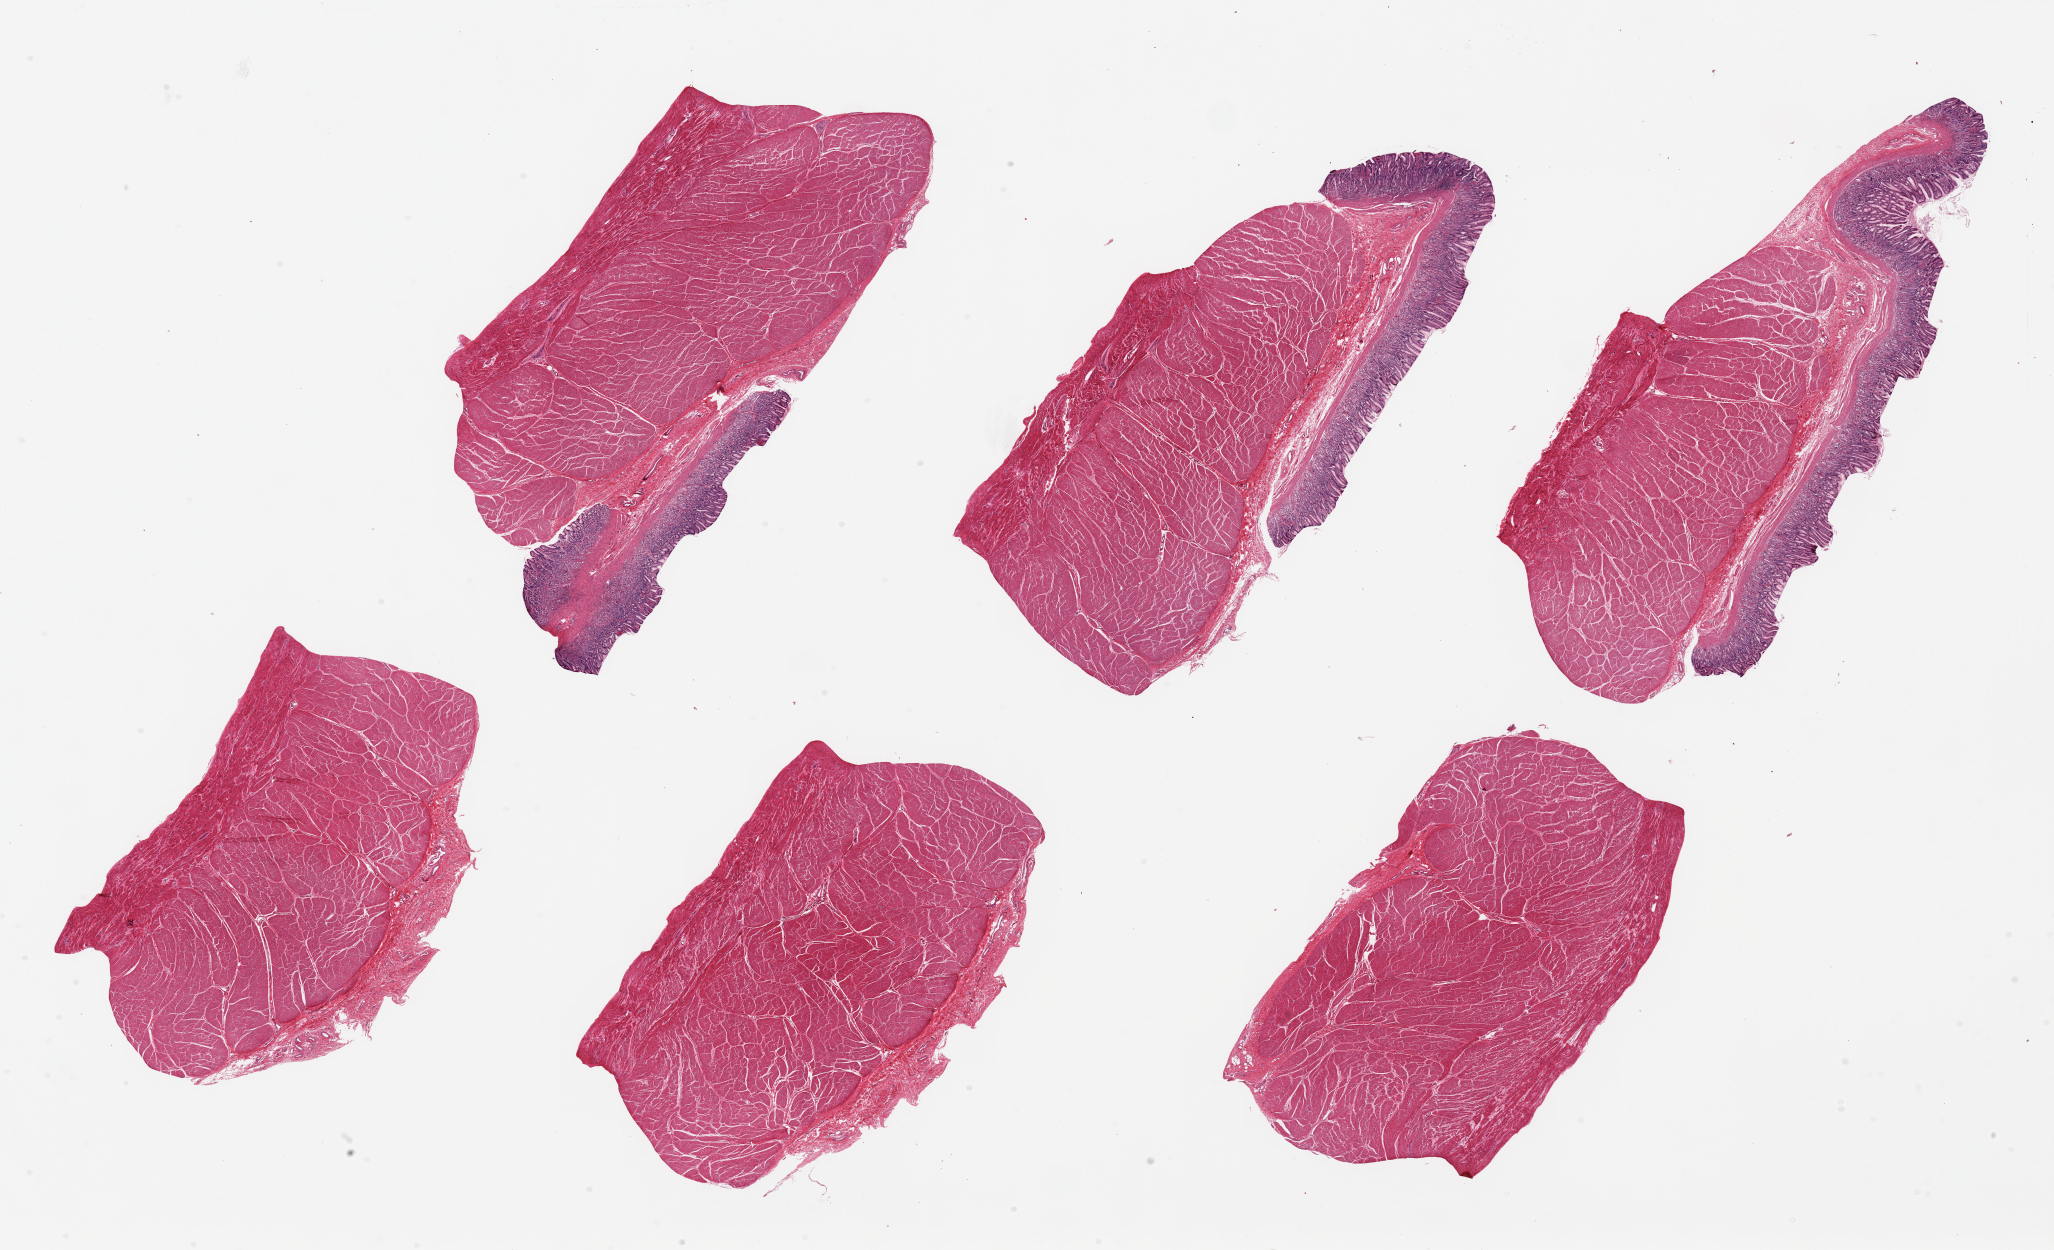
Whole-slide image, H&E stain — low-resolution overview of the scanned area, about 32.5 x 19.8 mm; PAXgene-fixed paraffin-embedded (PFPE) section; sampled site (target tissue): stomach; tissue donor sample. Donor: female.
- reviewer comment on this tissue sample: 6 pieces up to 10x4.8 mm; 3 have antral (not body) mucosa with mild chronic gastritis; 3 are only muscularis